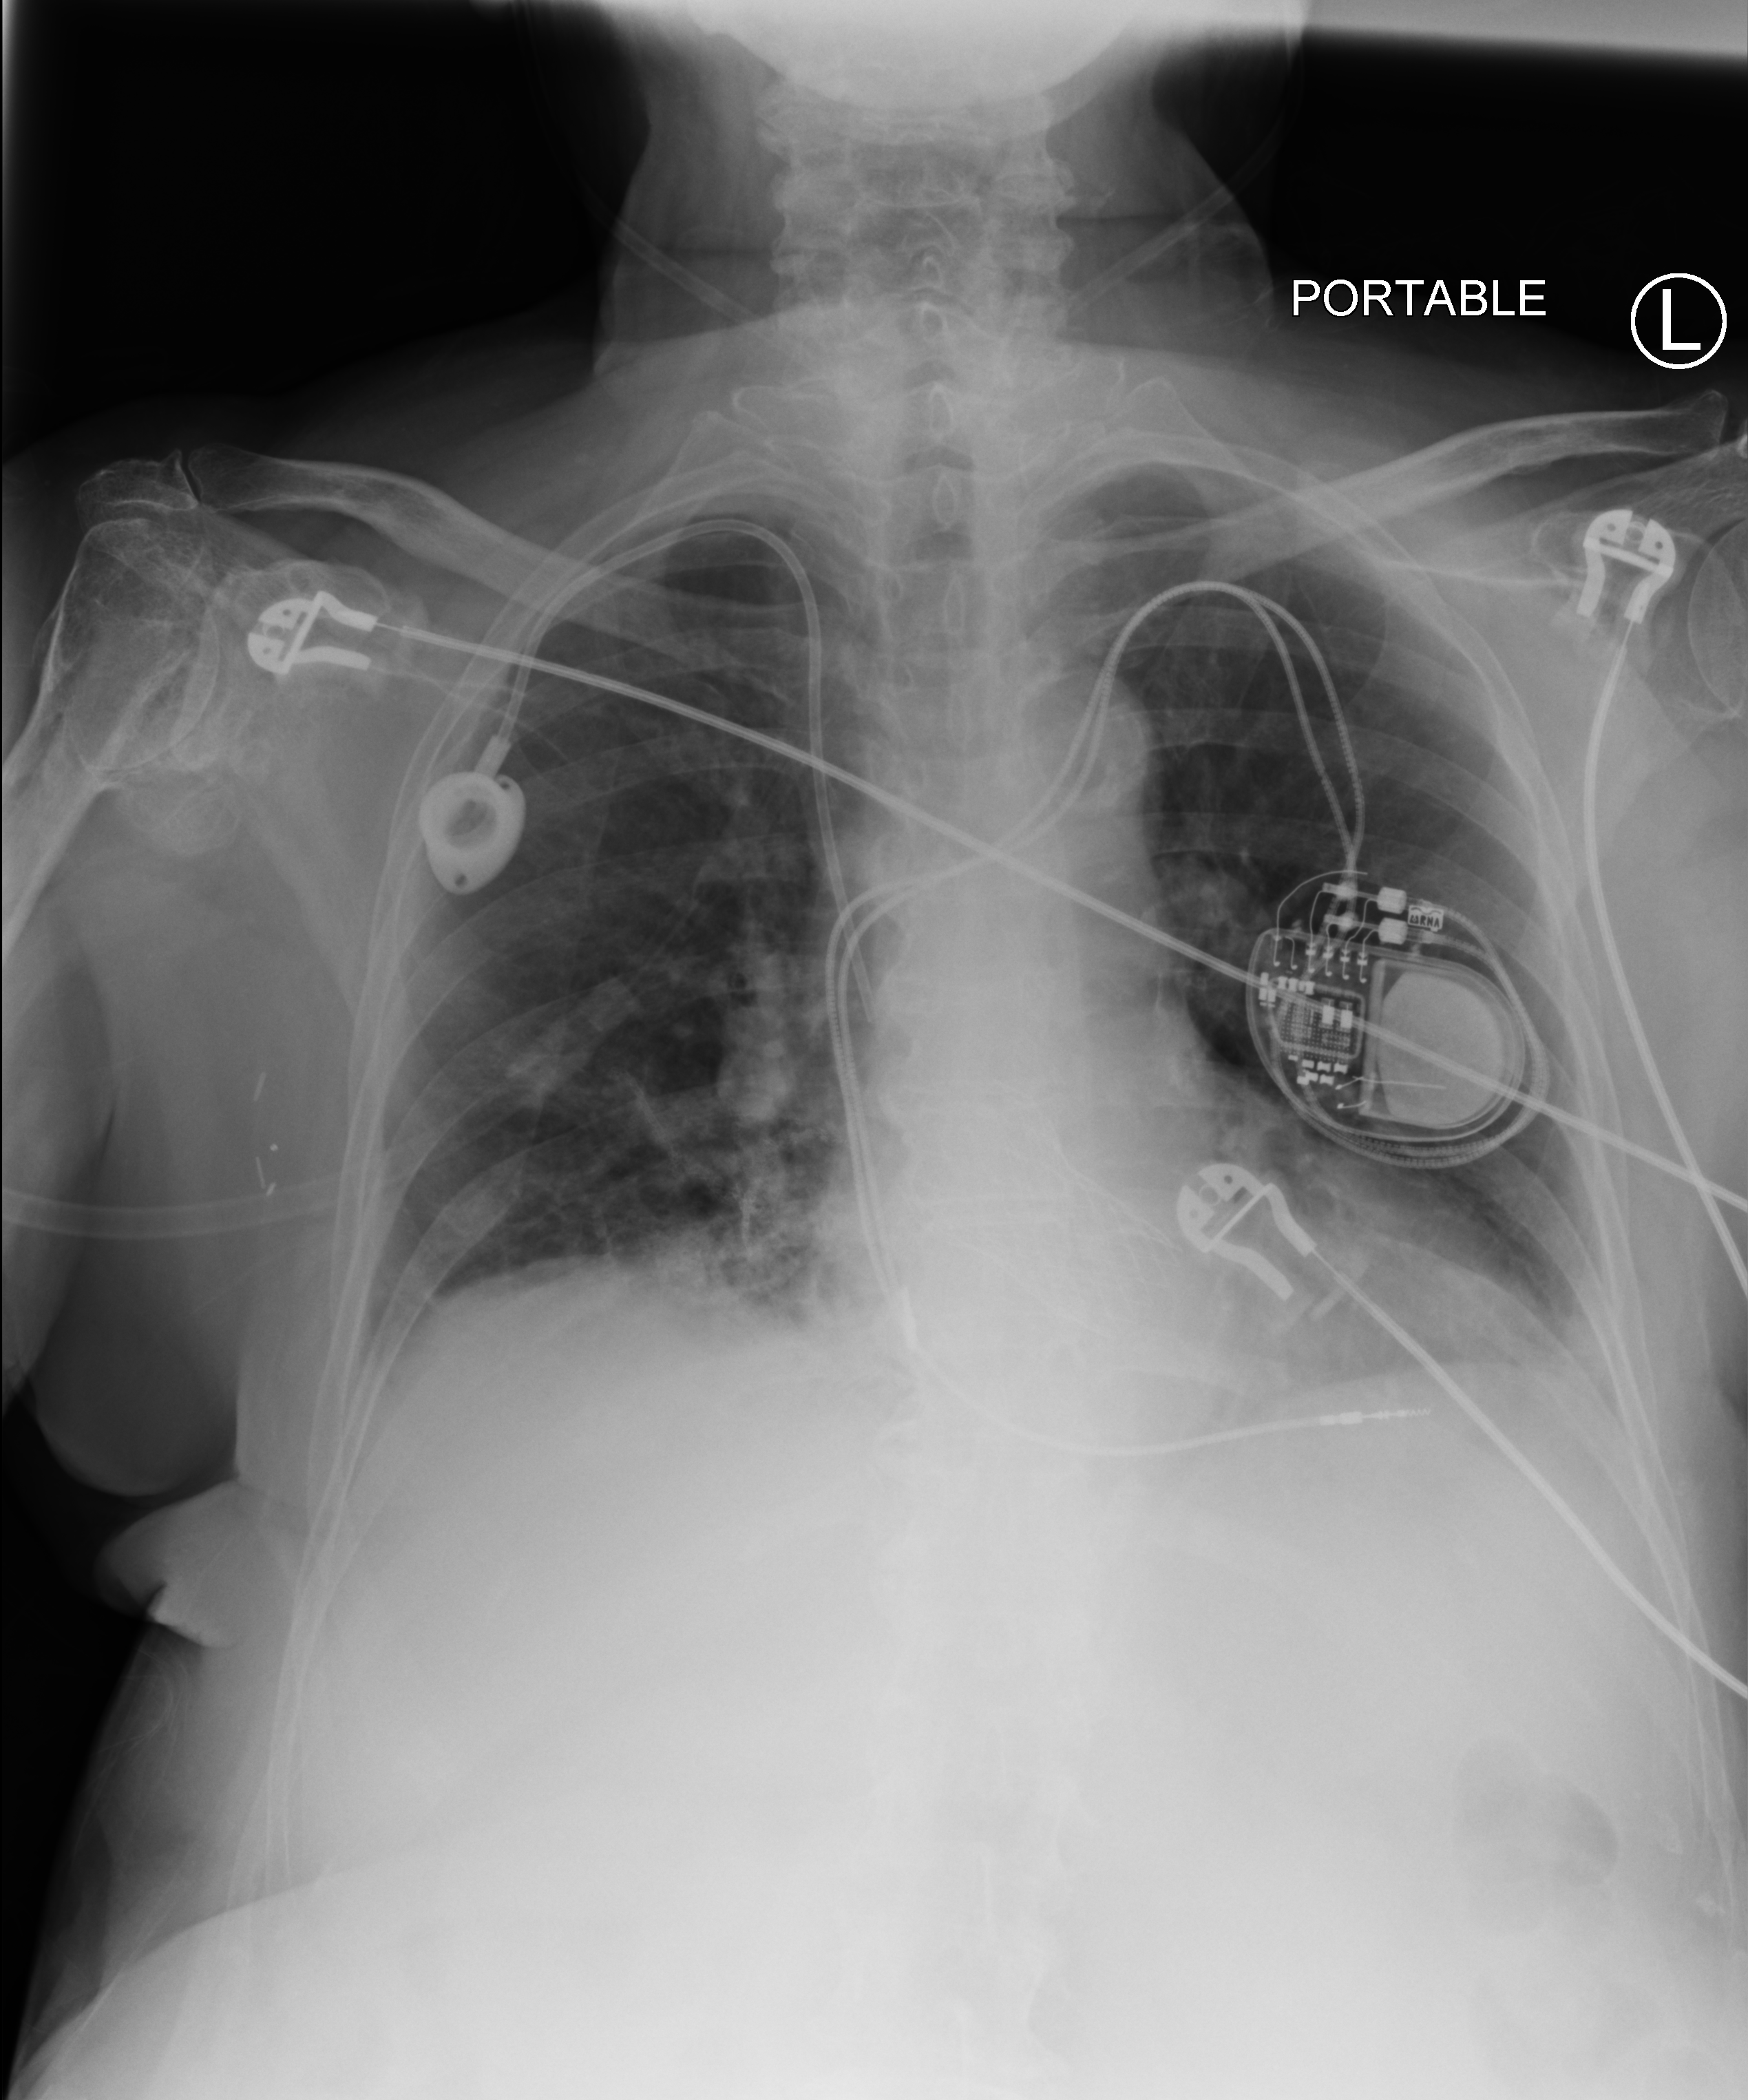
Portable chest radiograph. Female patient hospitalised with COVID-19, age 75–90 years.
Hospital-stay facts (about this admission, not read from this image; timing relative to this image not recorded):
- admitted to intensive care during this hospital stay: no